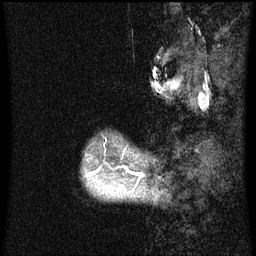
Breast MRI (dynamic contrast-enhanced), one sagittal slice; position 9 of 60 along the scan axis; dynamic contrast-enhanced series, image 2 of 3 at this slice position (ordered by acquisition); 1.5 T; TE 4.2 ms, TR 8 ms; 256 × 256 image matrix. Female patient, age 50 years.
Outlined on this slice (semi-automatically segmented with operator editing):
- analysis volume of interest (the breast-tissue region the enhancement analysis was run in; not a lesion): box from (x=86, y=144) to (x=142, y=198) px
- tumour enhancement mask (voxels above the 70 % enhancement threshold inside the analysis volume of interest): (x=128, y=171)–(x=131, y=193)